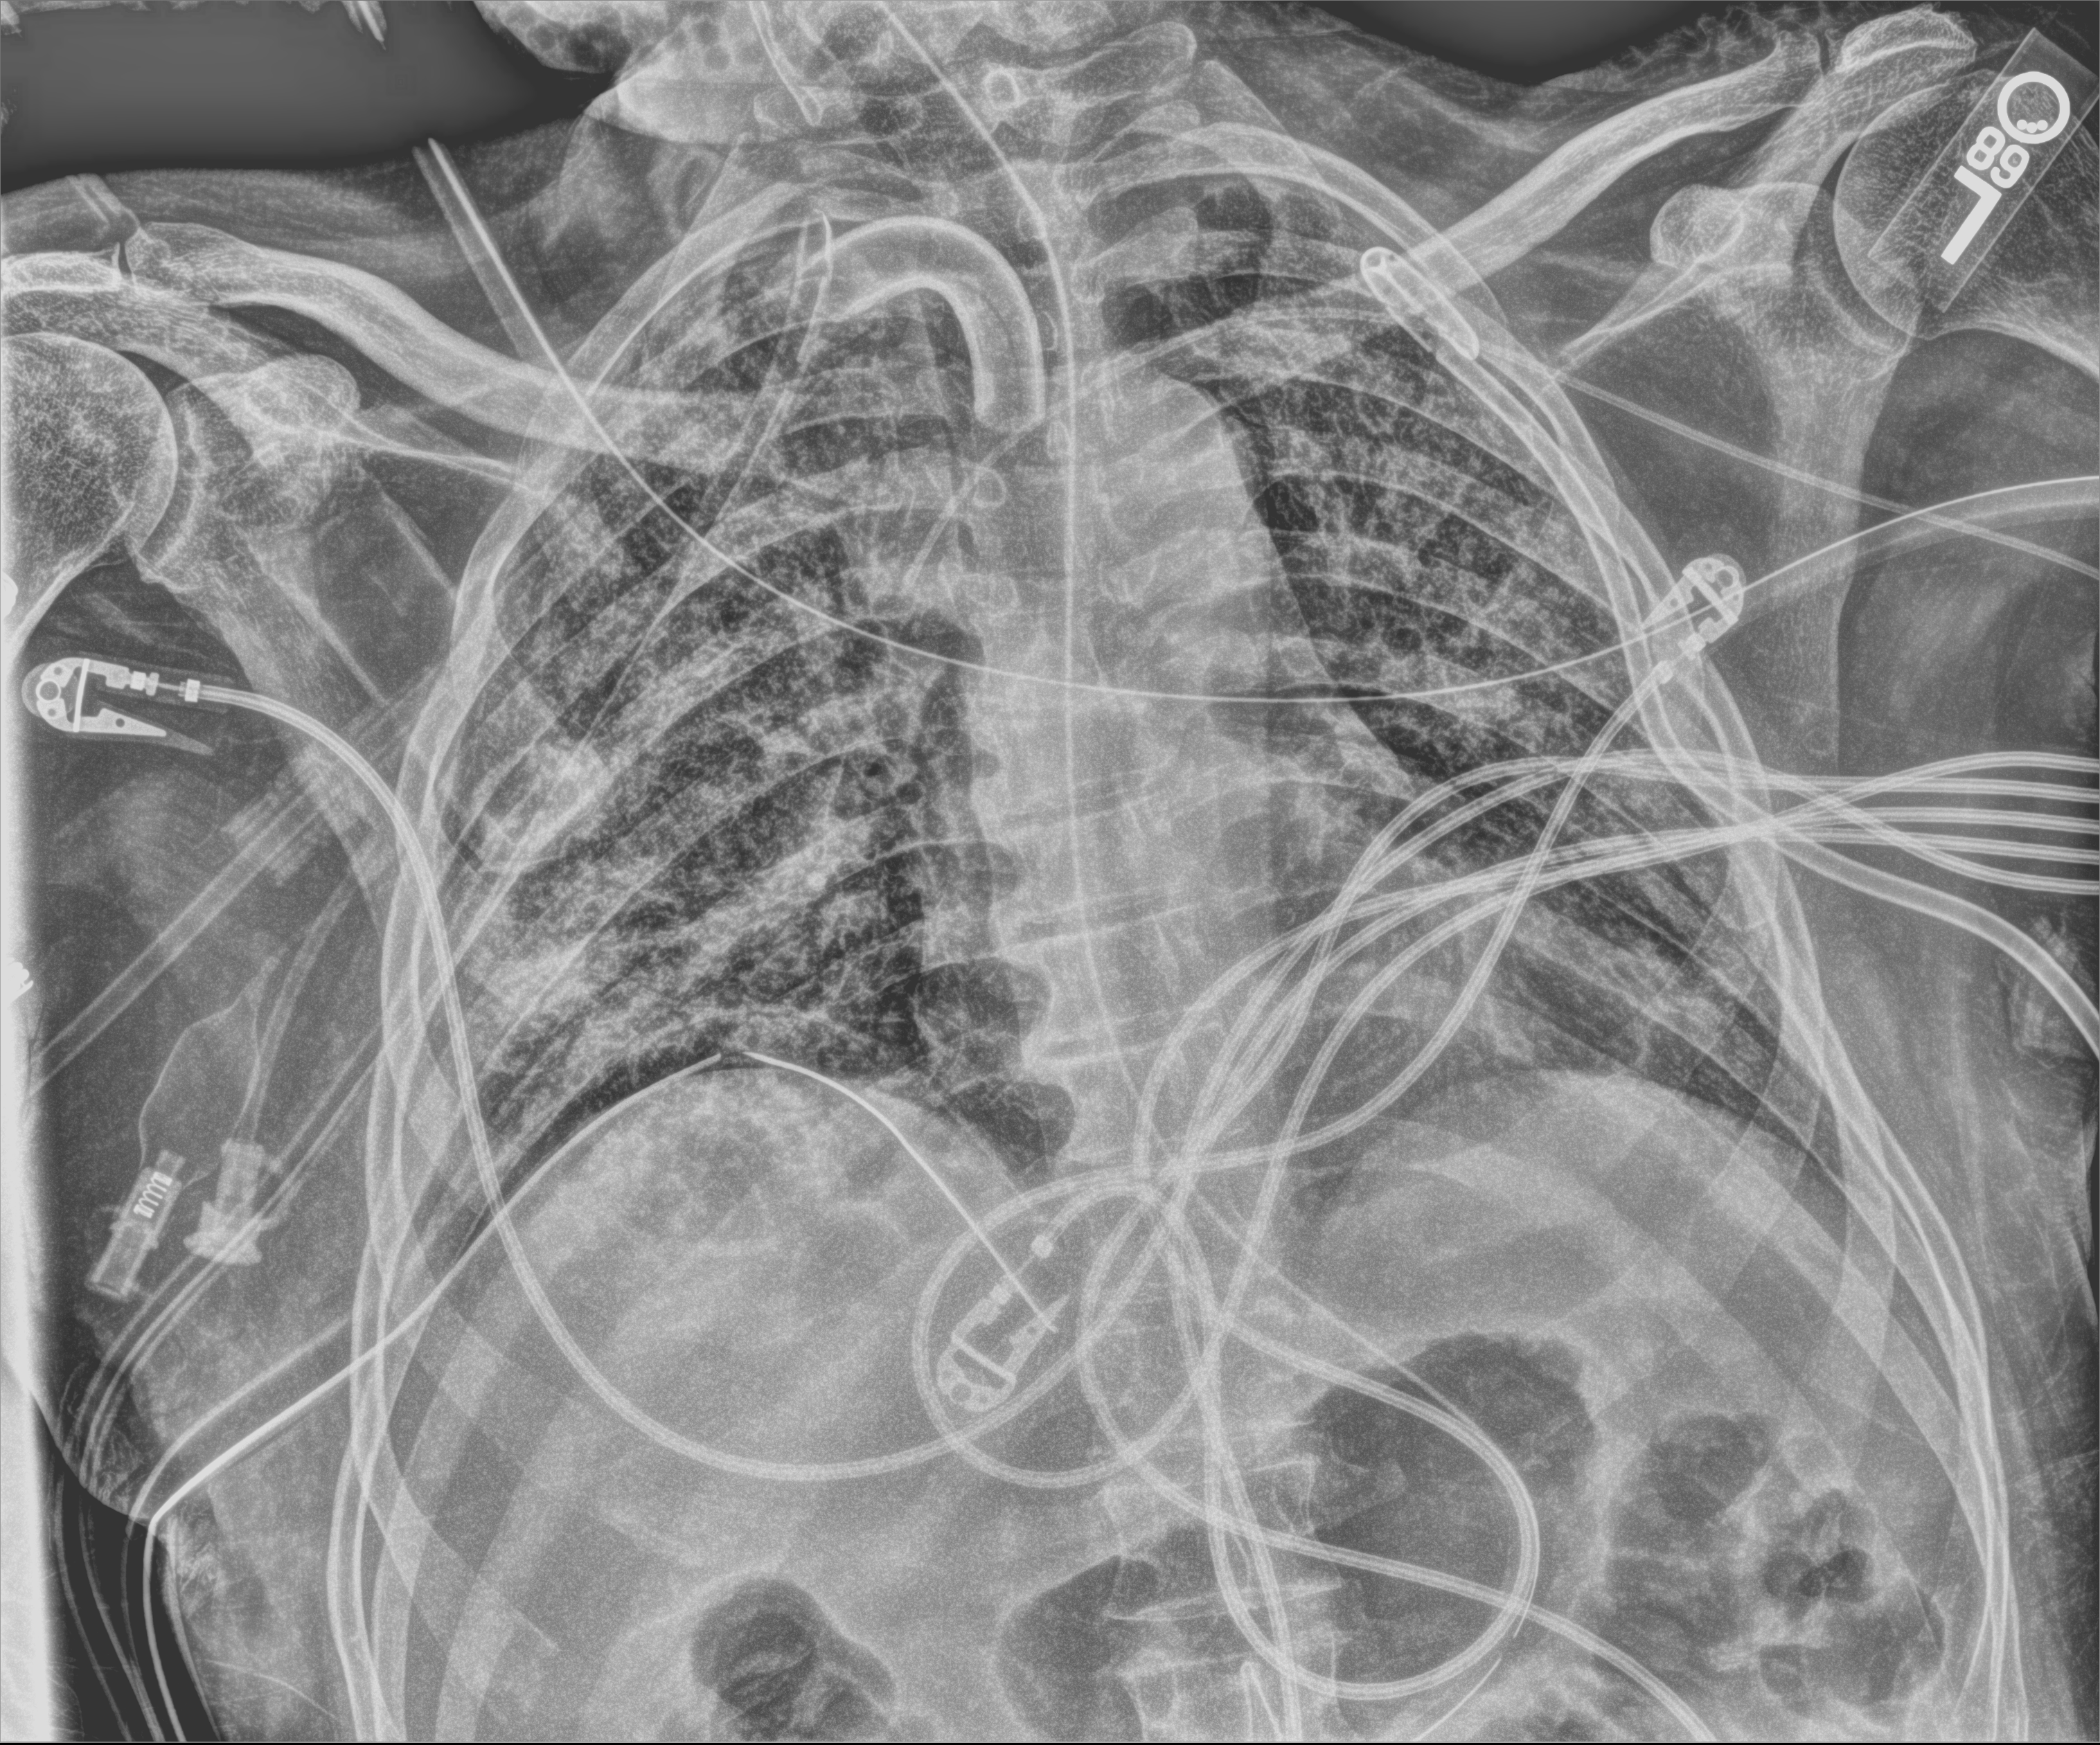
Chest X-ray (portable), anteroposterior (AP) projection. Patient hospitalised with COVID-19; male, aged 18–59 years.
Admission-level facts for this patient (not findings on this image; timing relative to this image not recorded): admitted to intensive care during this hospital stay: yes; COPD (admission record): no.